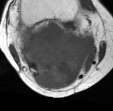
MRI of an extremity soft-tissue mass, one axial slice; MR volume resampled by the dataset authors to the PET/CT grid (not the native acquisition matrix); 3.27 mm slice thickness; 113 × 111 image matrix. Female patient. From the clinical record (not read from this slice): histological type: liposarcoma; site of the primary tumour: right thigh.
Annotated regions visible in this slice (expert contour drawn on MRI and transferred to this co-registered scan by the dataset authors):
- gross tumour volume (mass): bounding box (x1, y1, x2, y2) in pixels: (17, 20, 98, 88)